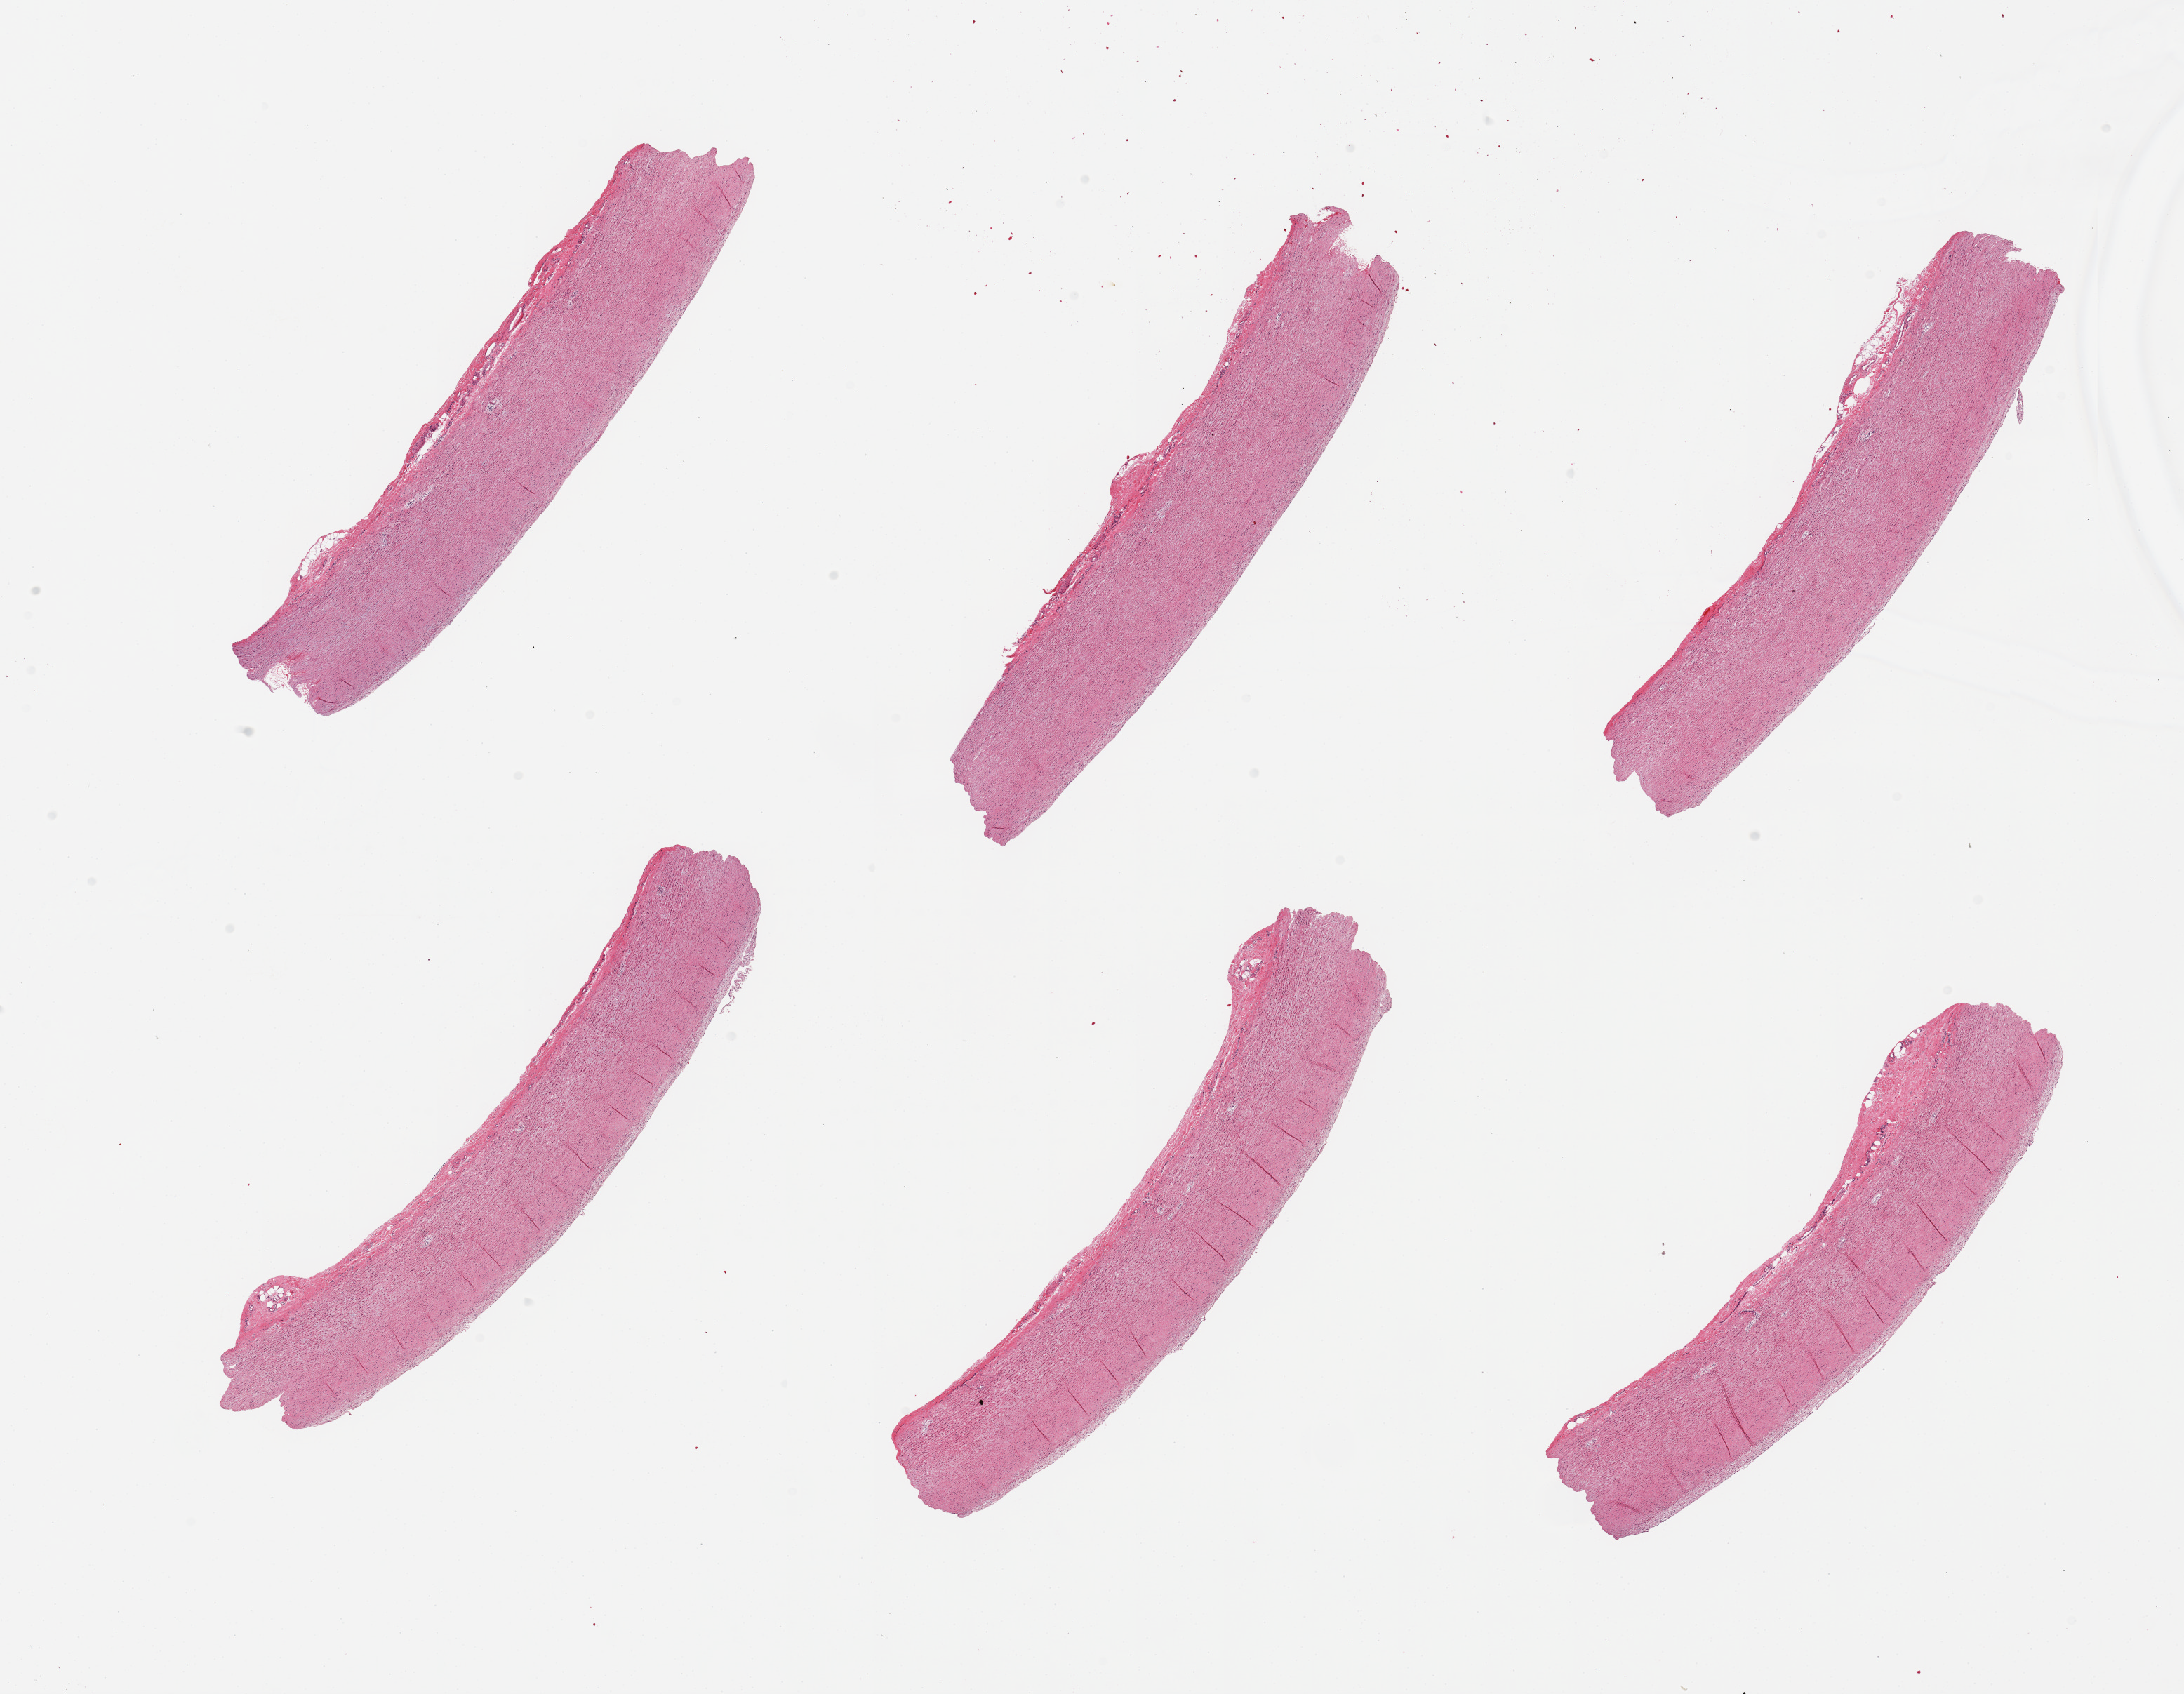
Whole-slide image, hematoxylin and eosin (H&E) stain, whole scanned area (about 24.6 x 19.1 mm) shown as a low-resolution overview; PAXgene-fixed, paraffin-embedded tissue; sampled site (target tissue): aorta; tissue donor sample. Donor sex: female.
Pathologist's review note for this sample: 6 pieces; intimal thickening.